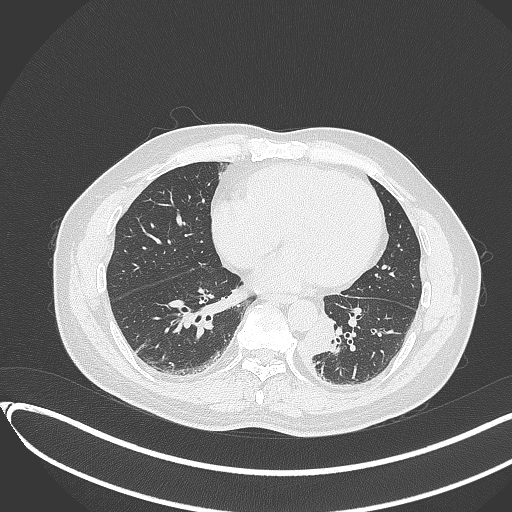
Chest CT, one axial slice; slice 122 of 417 in the series (ordered by position); reconstruction kernel B70f; lung window (W 1500 / L -600 HU); 1 mm slice thickness; 512 × 512 image matrix. Patient: male, 54 years. From the clinical record (not read from this slice): clinical TNM (as recorded): T3 N0 M0.
Structures marked on this image (bounding box drawn by a radiologist):
- lung tumour (recorded histology: squamous cell carcinoma): bounding box <303,313,338,359> (left, top, right, bottom; pixels)